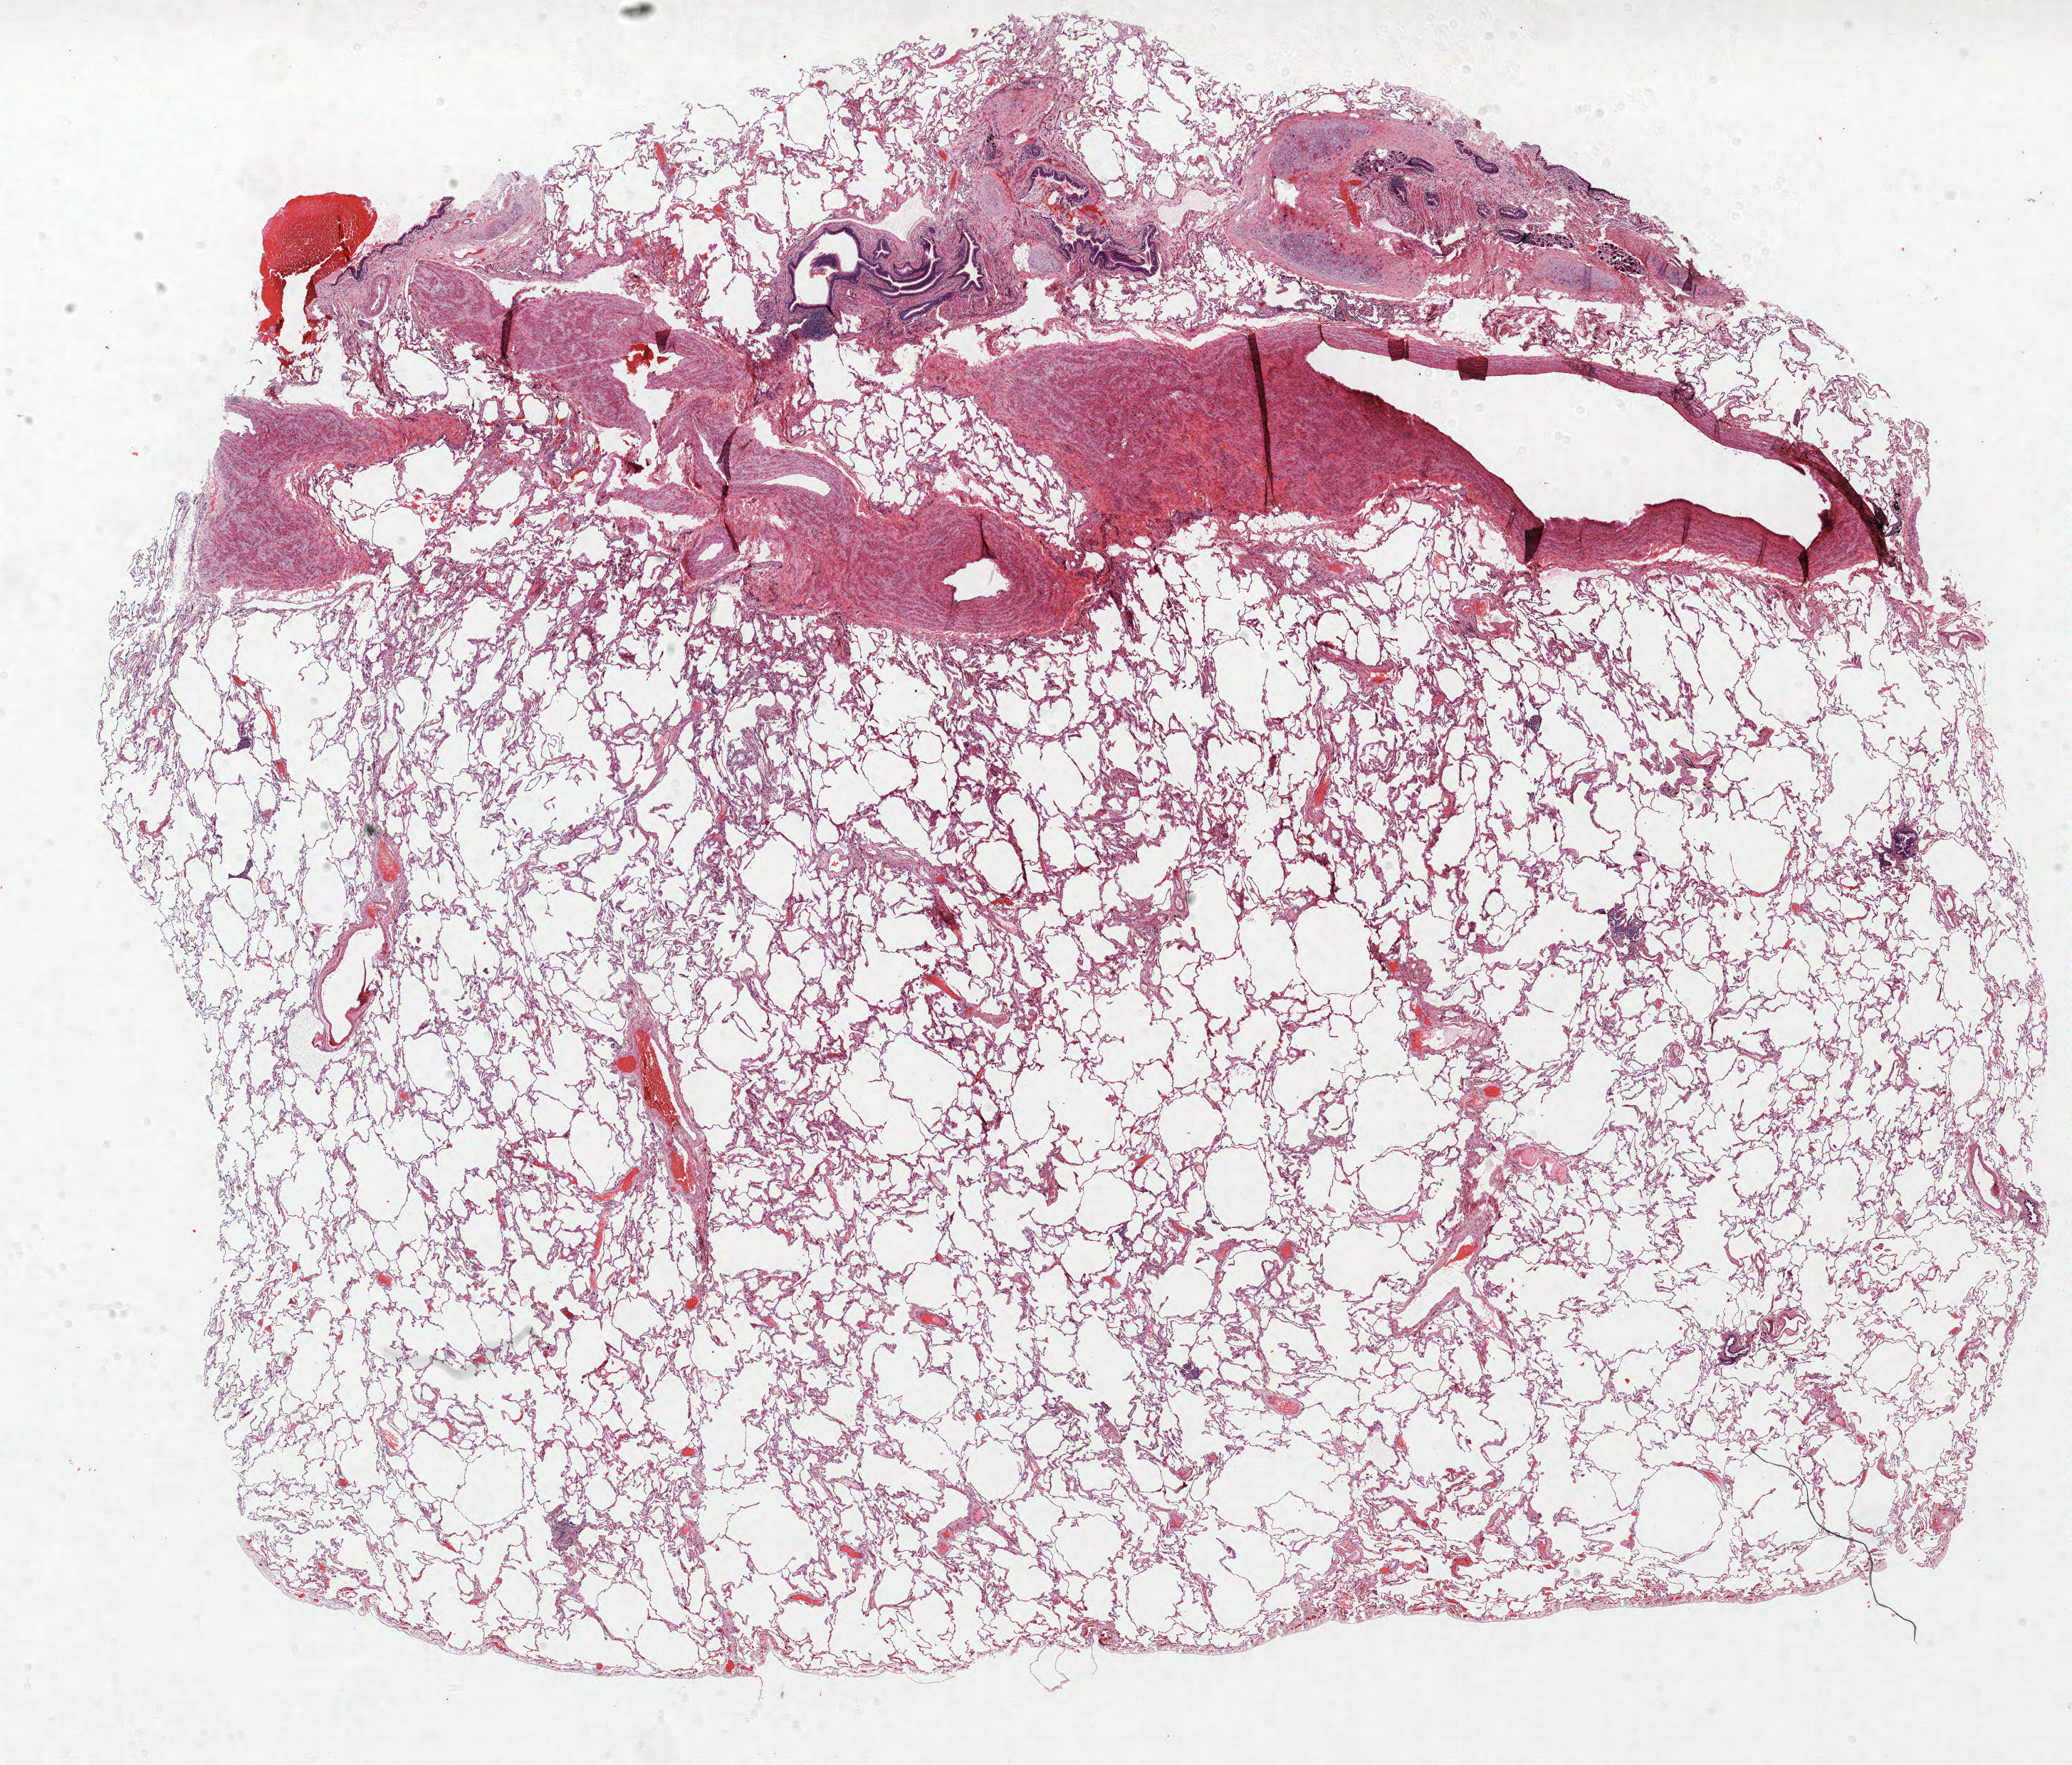
H&E whole-slide image, shown as a low-resolution overview of the whole scanned area (about 23.3 x 19.8 mm, slide scanned at 40x); formalin-fixed paraffin-embedded (FFPE) section; lung. Female, age 58 at enrolment. Former smoker at enrolment. Grade: moderately differentiated (G2).
Primary tumour location (clinical record): left upper lobe. Stage (AJCC 6th edition): IIA. Tumour size (pathology): 15 mm. Participant's lung-cancer diagnosis: Adenocarcinoma, NOS (ICD-O-3 8140/3).